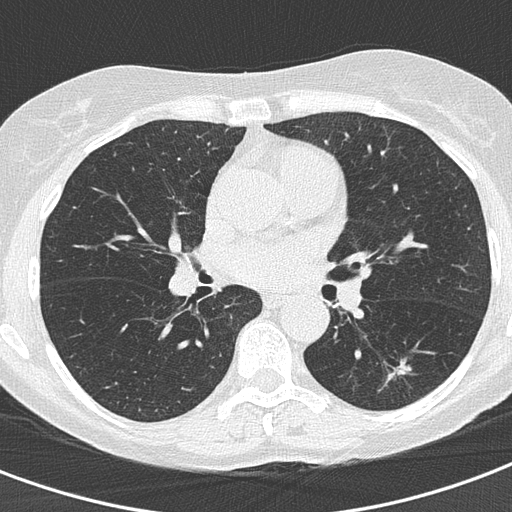
Chest CT (low-dose screening protocol), one axial image. Second annual screen. Lung window (W 1500 / L -600 HU). 2 mm slice thickness. Lung (sharp) reconstruction kernel (B50f). Slice 73 of 155 in the series. Female participant, aged 60 years at enrolment. Current smoker at enrolment.
Expert-annotated lung lesion, bounding box (x1, y1, x2, y2) in pixels: (378, 350, 416, 381). The exam's reader record, not a measurement of the box and not confirmed to be the same lesion: non-calcified nodule or mass ≥4 mm, left lower lobe, 10 × 9 mm, soft tissue attenuation. Official screen result: positive, other. Lung cancer was diagnosed 64 days after this screen: adenocarcinoma, NOS, left lower lobe, well differentiated (G1), stage IA (AJCC 6th edition), 15 mm at pathology.